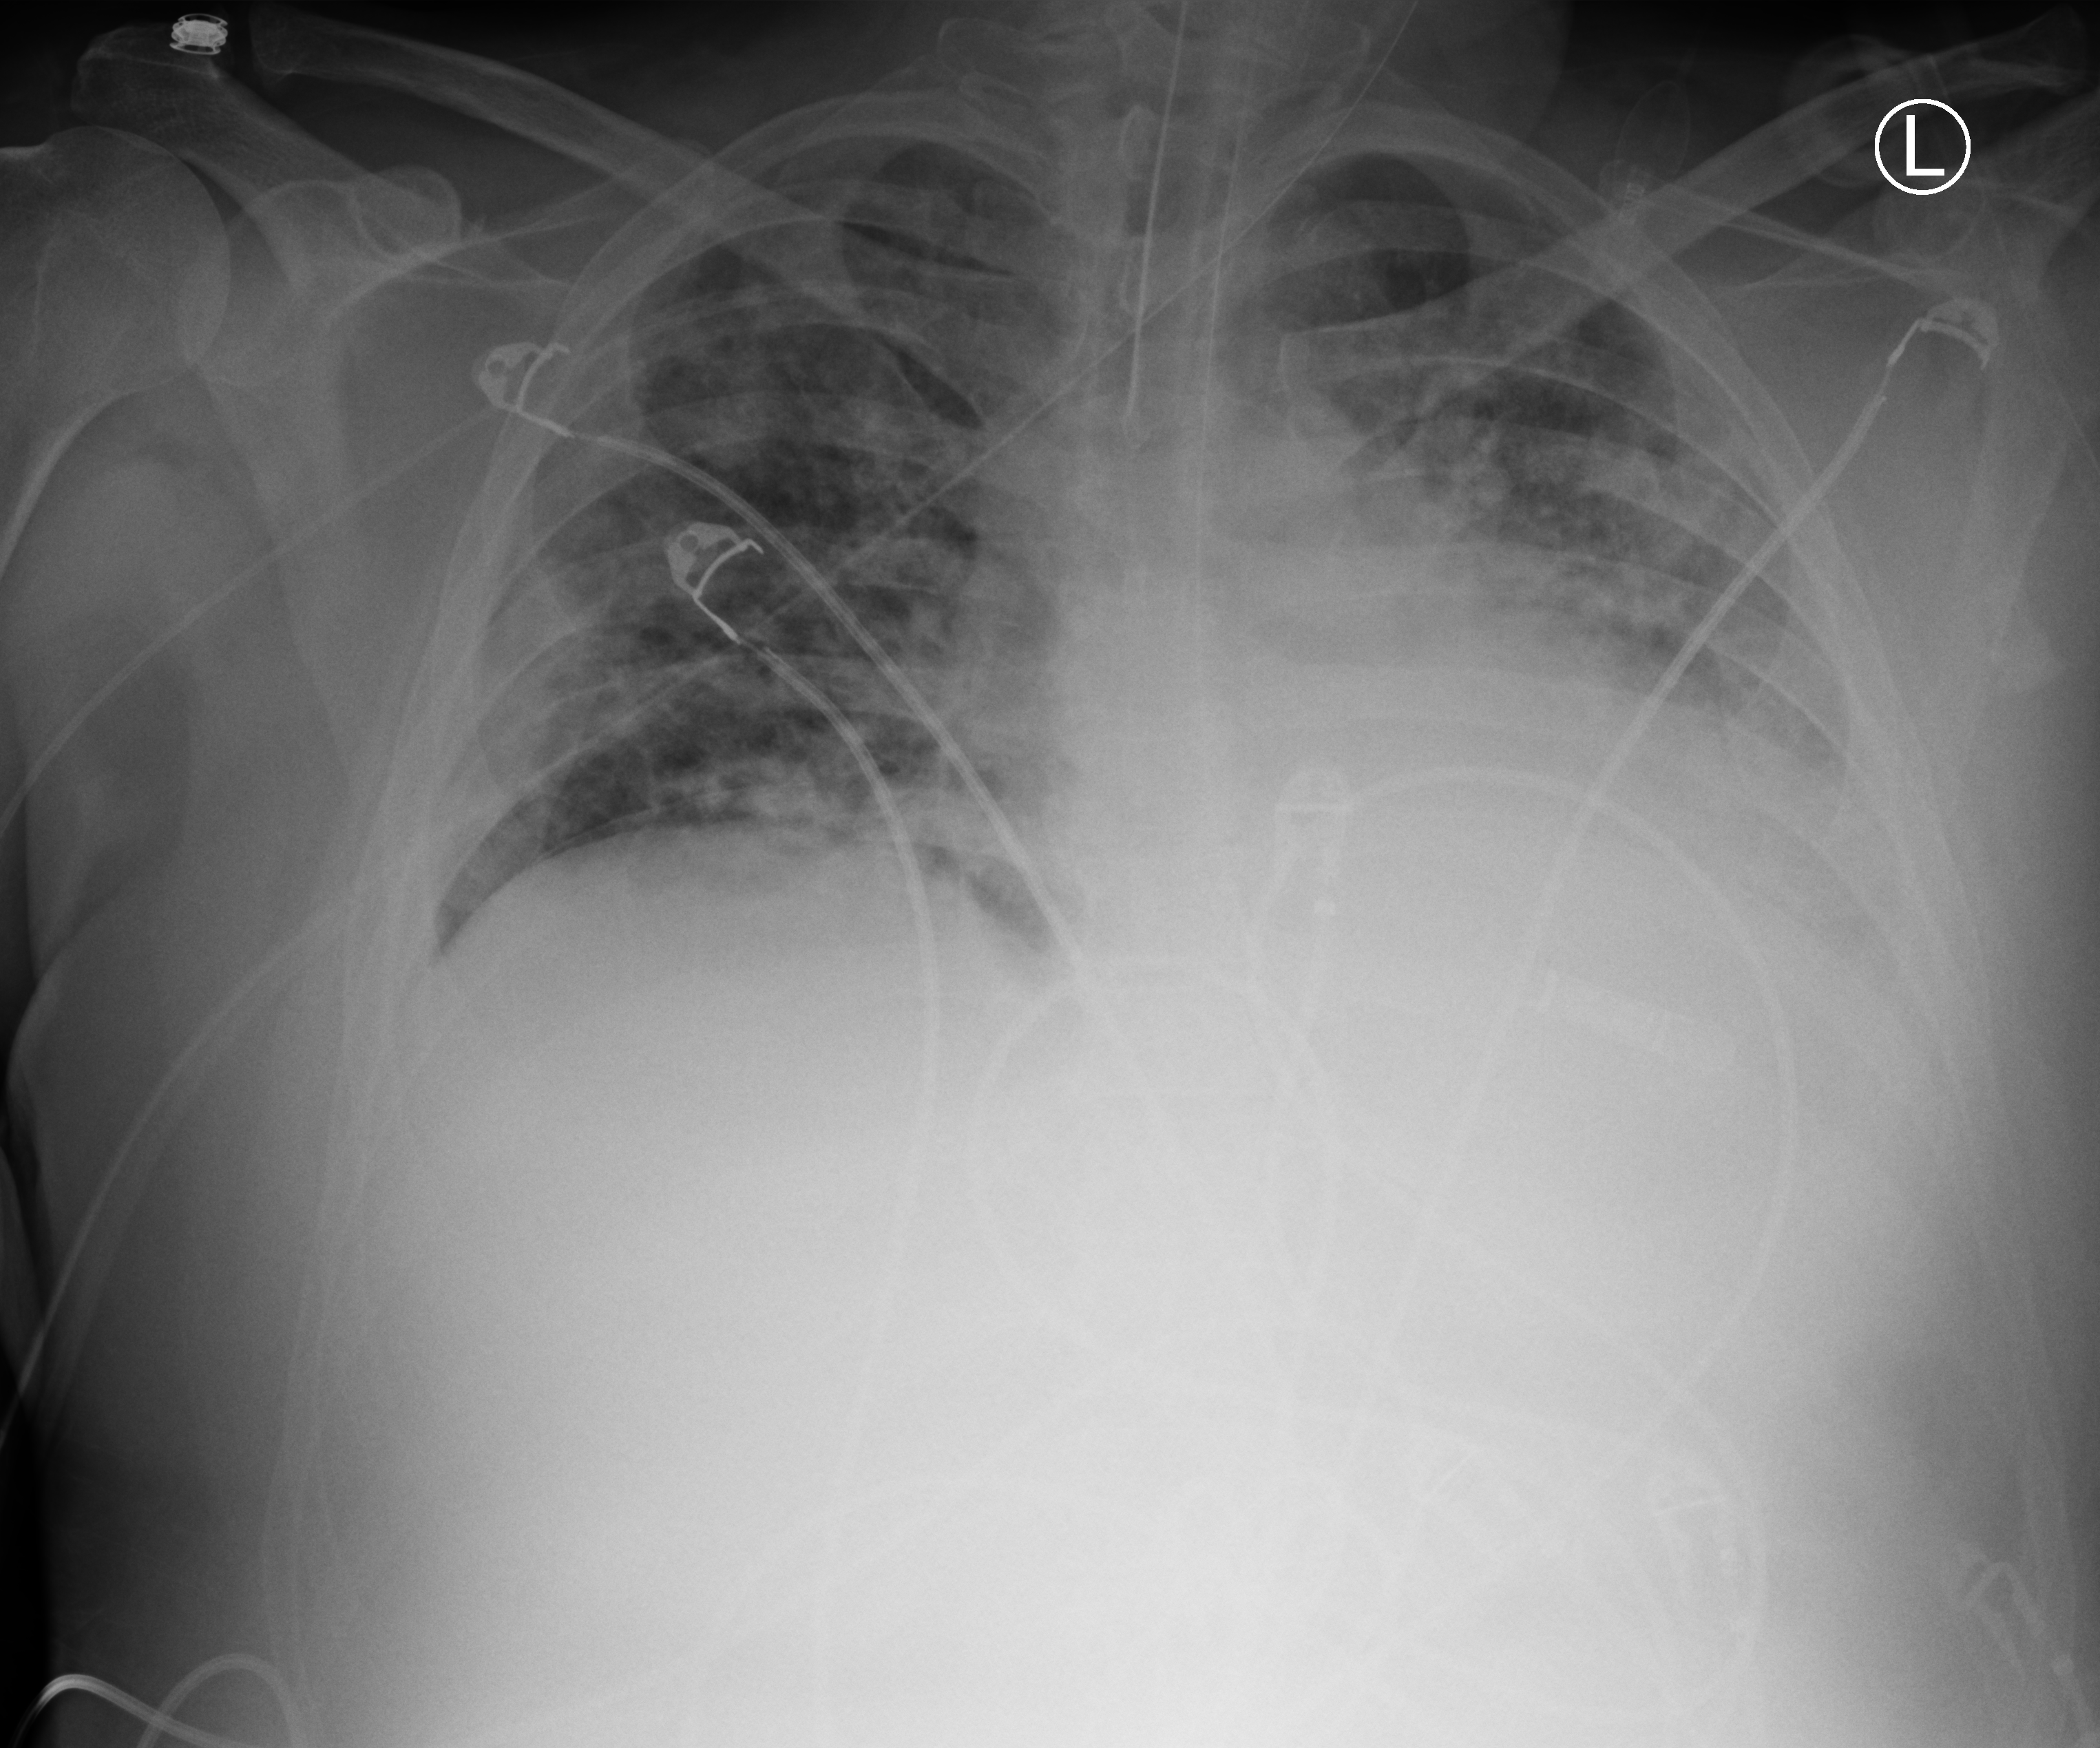
Bedside chest radiograph (computed radiography); anteroposterior (AP) projection. Male patient hospitalised with COVID-19, age 18–59 years.
Hospital-stay facts (about this admission, not read from this image; timing relative to this image not recorded): admitted to intensive care during this hospital stay: yes; length of hospital stay: 39 days.